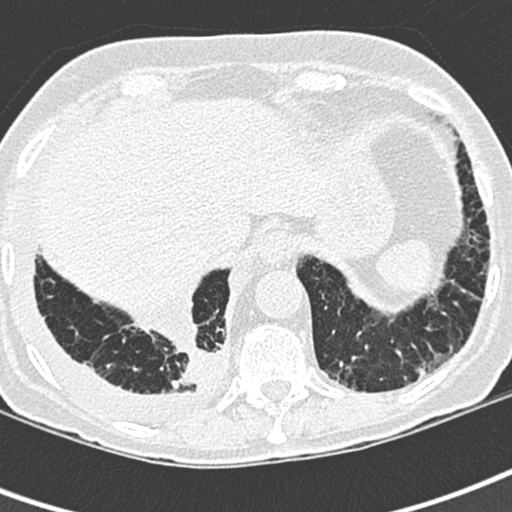
Low-dose screening chest CT, one axial slice; position 63 of 220 along the scan axis; 120 kVp; lung window (W 1500 / L -600 HU); 1.3 mm slice thickness; 512 × 512 image matrix.
Structures marked on this image (manually delineated by an expert):
- lesion 1 (tumor, lower lobe of right lung): bounding box <180,349,218,385> (left, top, right, bottom; pixels)
- lesion 2 (nodule, lower lobe of left lung): <418,366,428,376>